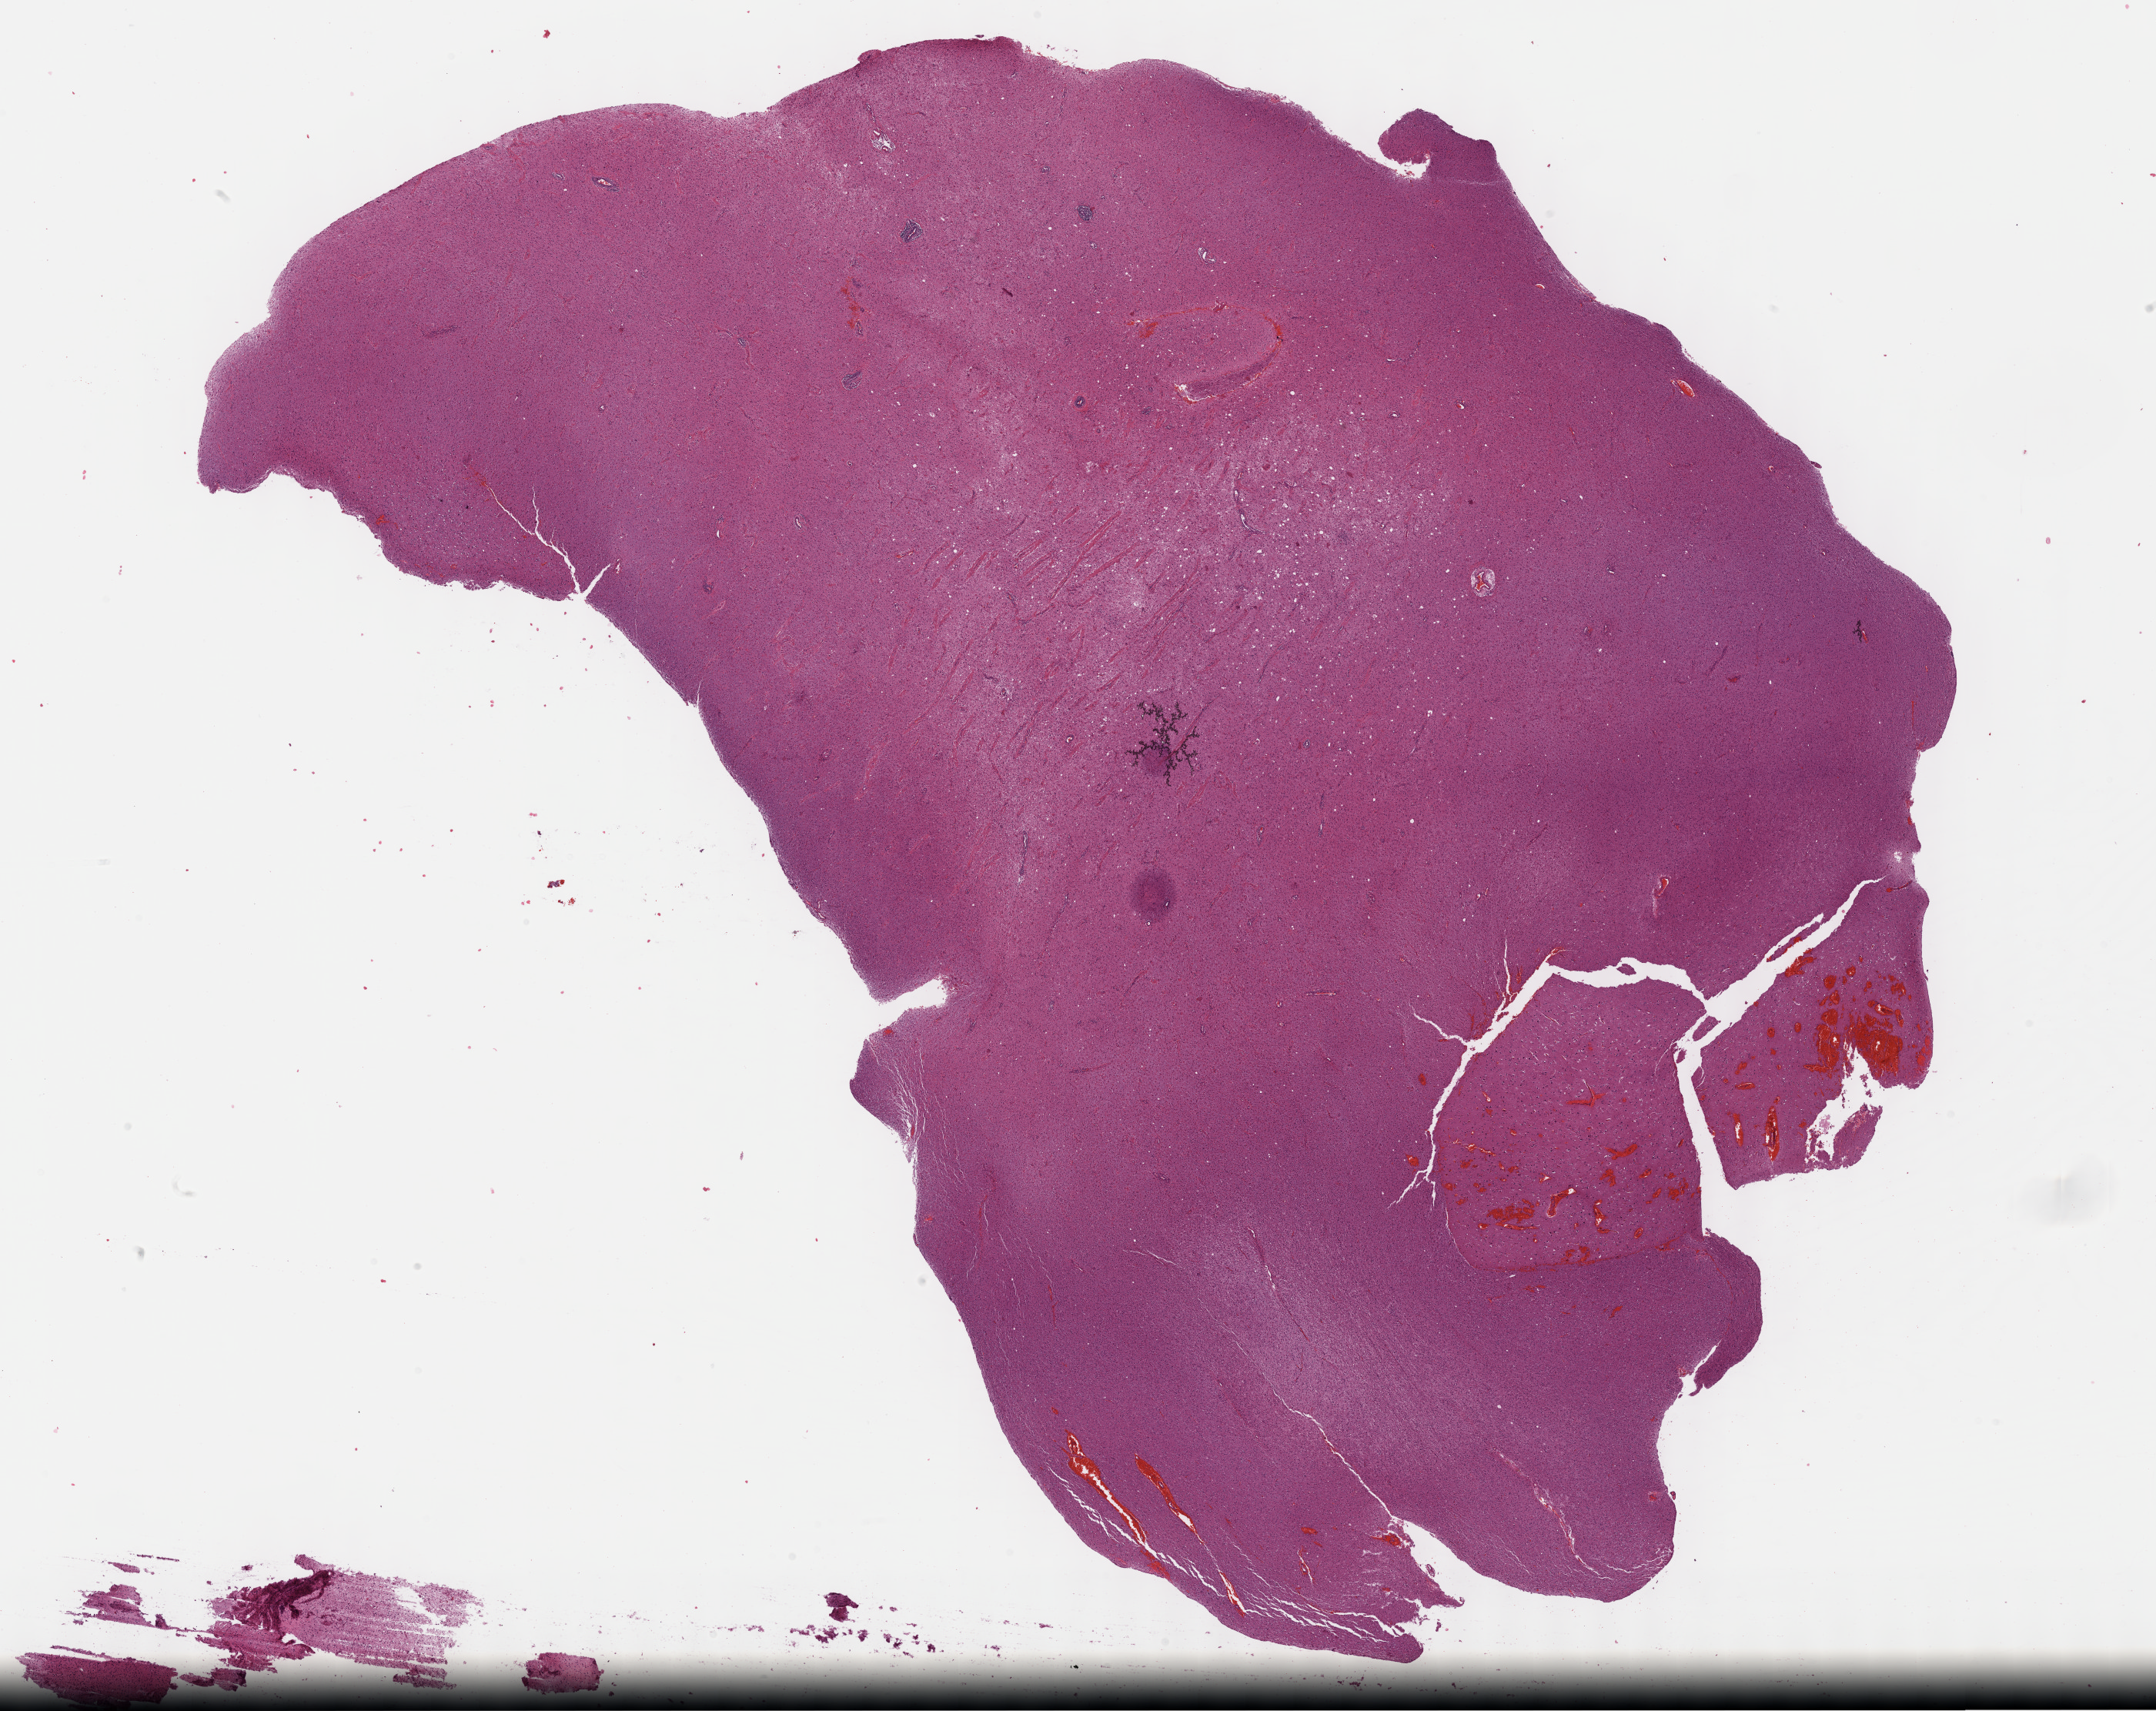
H&E whole-slide image, low-resolution overview of the scanned area, about 22.7 x 18.0 mm (slide scanned at 40x), formalin-fixed paraffin-embedded (FFPE) diagnostic section, primary tumour sample from the brain. Male, age 34 years at initial diagnosis. Histologic grade: G3 (poorly differentiated).
Diagnosis: Mixed glioma (cerebrum). Laterality: right.